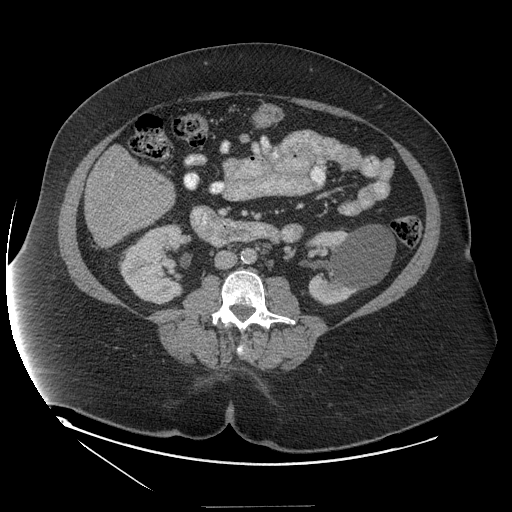
Contrast-enhanced abdominal CT (liver protocol), one axial slice. Position 36 of 127 along the scan axis. Reconstruction kernel STANDARD. 140 kVp. Soft-tissue window (W 400 / L 40 HU). 512 × 512 image matrix, field of view 480 × 480 mm. Case-level facts recorded for this patient, not image findings: diagnosis: hepatocellular carcinoma (patient treated with transarterial chemoembolisation; whether this scan precedes or follows treatment is not stated here); TNM stage (as recorded): Stage-II; Child-Pugh class: A; tumour differentiation: well differentiated; tumour nodularity: multinodular.
Annotated regions visible in this slice (semi-automatically segmented with operator editing):
- liver parenchyma outside the tumour (the mass and vessels are separate outlines, so this box may not span the whole liver): bounding box [x1, y1, x2, y2] px = [84, 178, 174, 246]